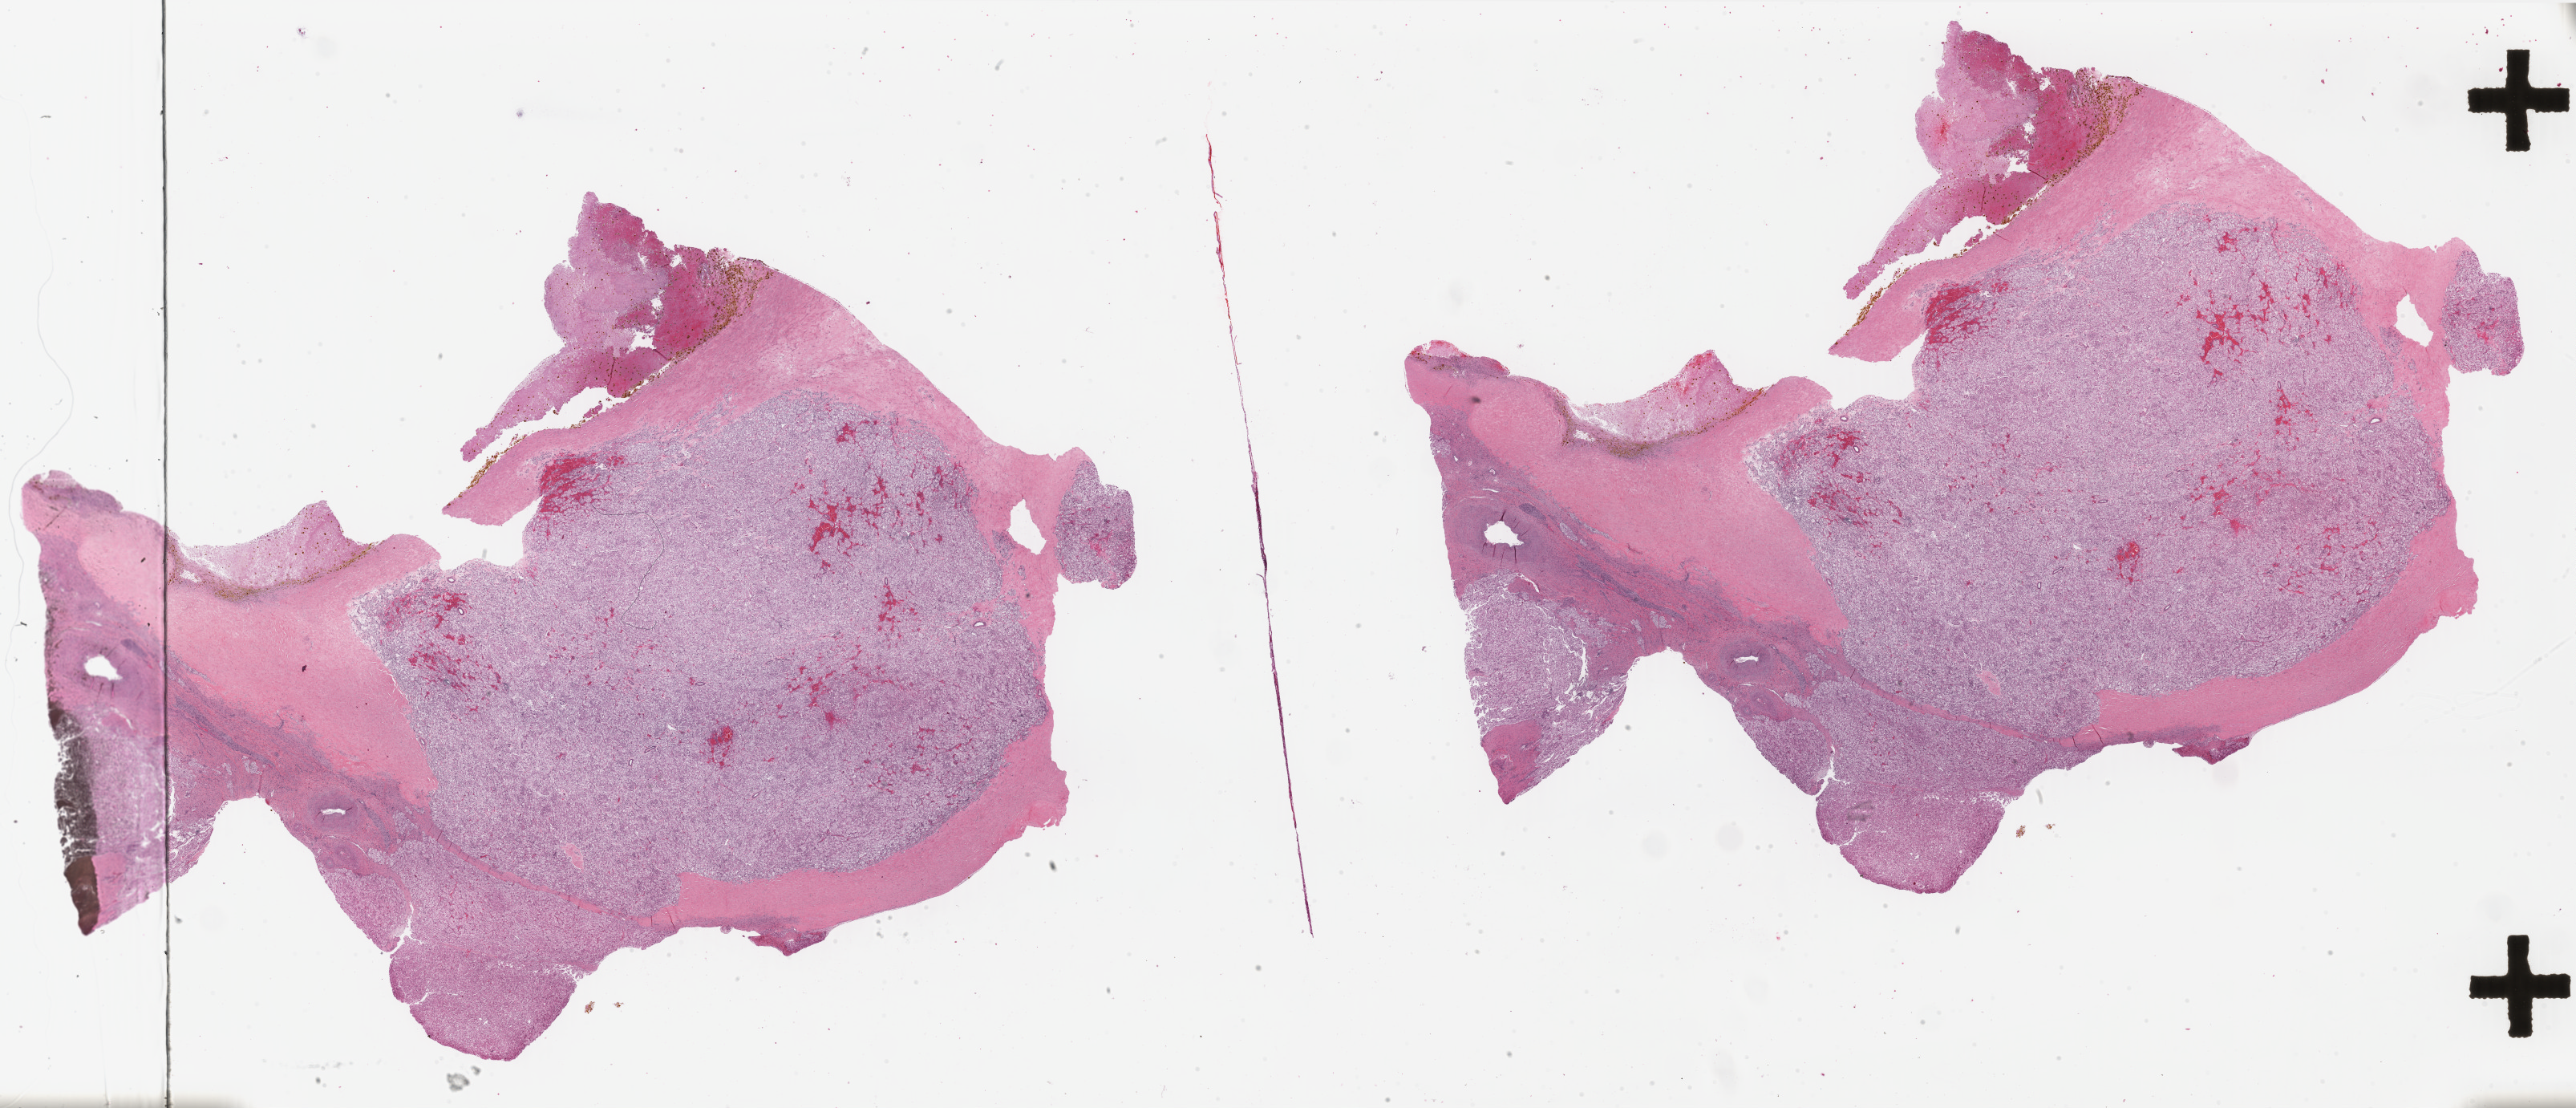
Whole-slide histology image, H&E-stained, low-resolution overview of the scanned area, about 50.8 x 21.9 mm; formalin-fixed paraffin-embedded (FFPE) diagnostic section; sample: primary tumour, kidney. Female patient; age at initial diagnosis 43 years.
Laterality: left. Pathologic diagnosis: Renal cell carcinoma, chromophobe type. TNM: T1b NX. AJCC pathologic stage: I (7th edition).